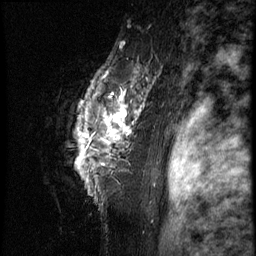
Breast MRI (dynamic contrast-enhanced), one sagittal slice. Position 57 of 66 along the scan axis. 3 images stored at this slice position (order not interpretable as contrast timing). 1.5 T. TE 4.2 ms, TR 8.9 ms. 2.5 mm slice thickness. 256 × 256 image matrix, field of view 200 × 200 mm. Female patient, age 39 years. Case-level facts recorded for this patient, not image findings: setting: breast cancer imaged before/during neoadjuvant chemotherapy; receptor status: HER2-positive.
Annotated regions visible in this slice (semi-automatic segmentation, software-assisted and operator-edited):
- analysis volume of interest (the breast-tissue region the enhancement analysis was run in; not a lesion): bounding box [x1, y1, x2, y2] px = [44, 44, 166, 196]
- tumour enhancement mask (voxels above the 140 % enhancement threshold inside the analysis volume of interest): [78, 81, 145, 163]